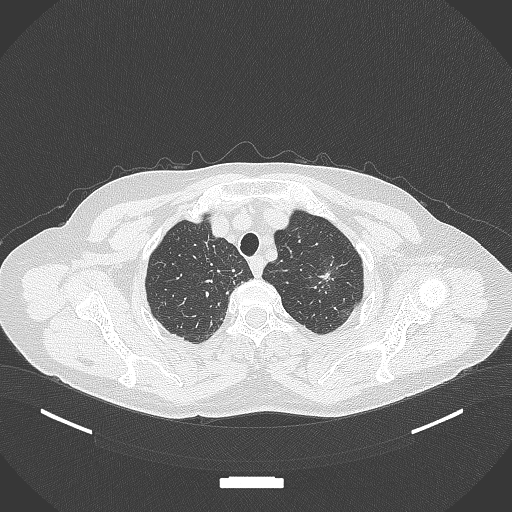
Chest CT, one axial slice. Position 310 of 369 along the scan axis. Reconstruction kernel B70f. 120 kVp. Lung window (W 1500 / L -600 HU). 1 mm slice thickness. 512 × 512 image matrix, field of view 400 × 400 mm. Patient: female, 64 years. Case-level facts recorded for this patient, not image findings: clinical TNM (as recorded): T1c N0 M0; histopathological grade: G1.
Outlined on this slice (rectangle marked by the reading radiologist):
- lung tumour (recorded histology: adenocarcinoma): bounding box (x1, y1, x2, y2) in pixels: (308, 248, 348, 300)